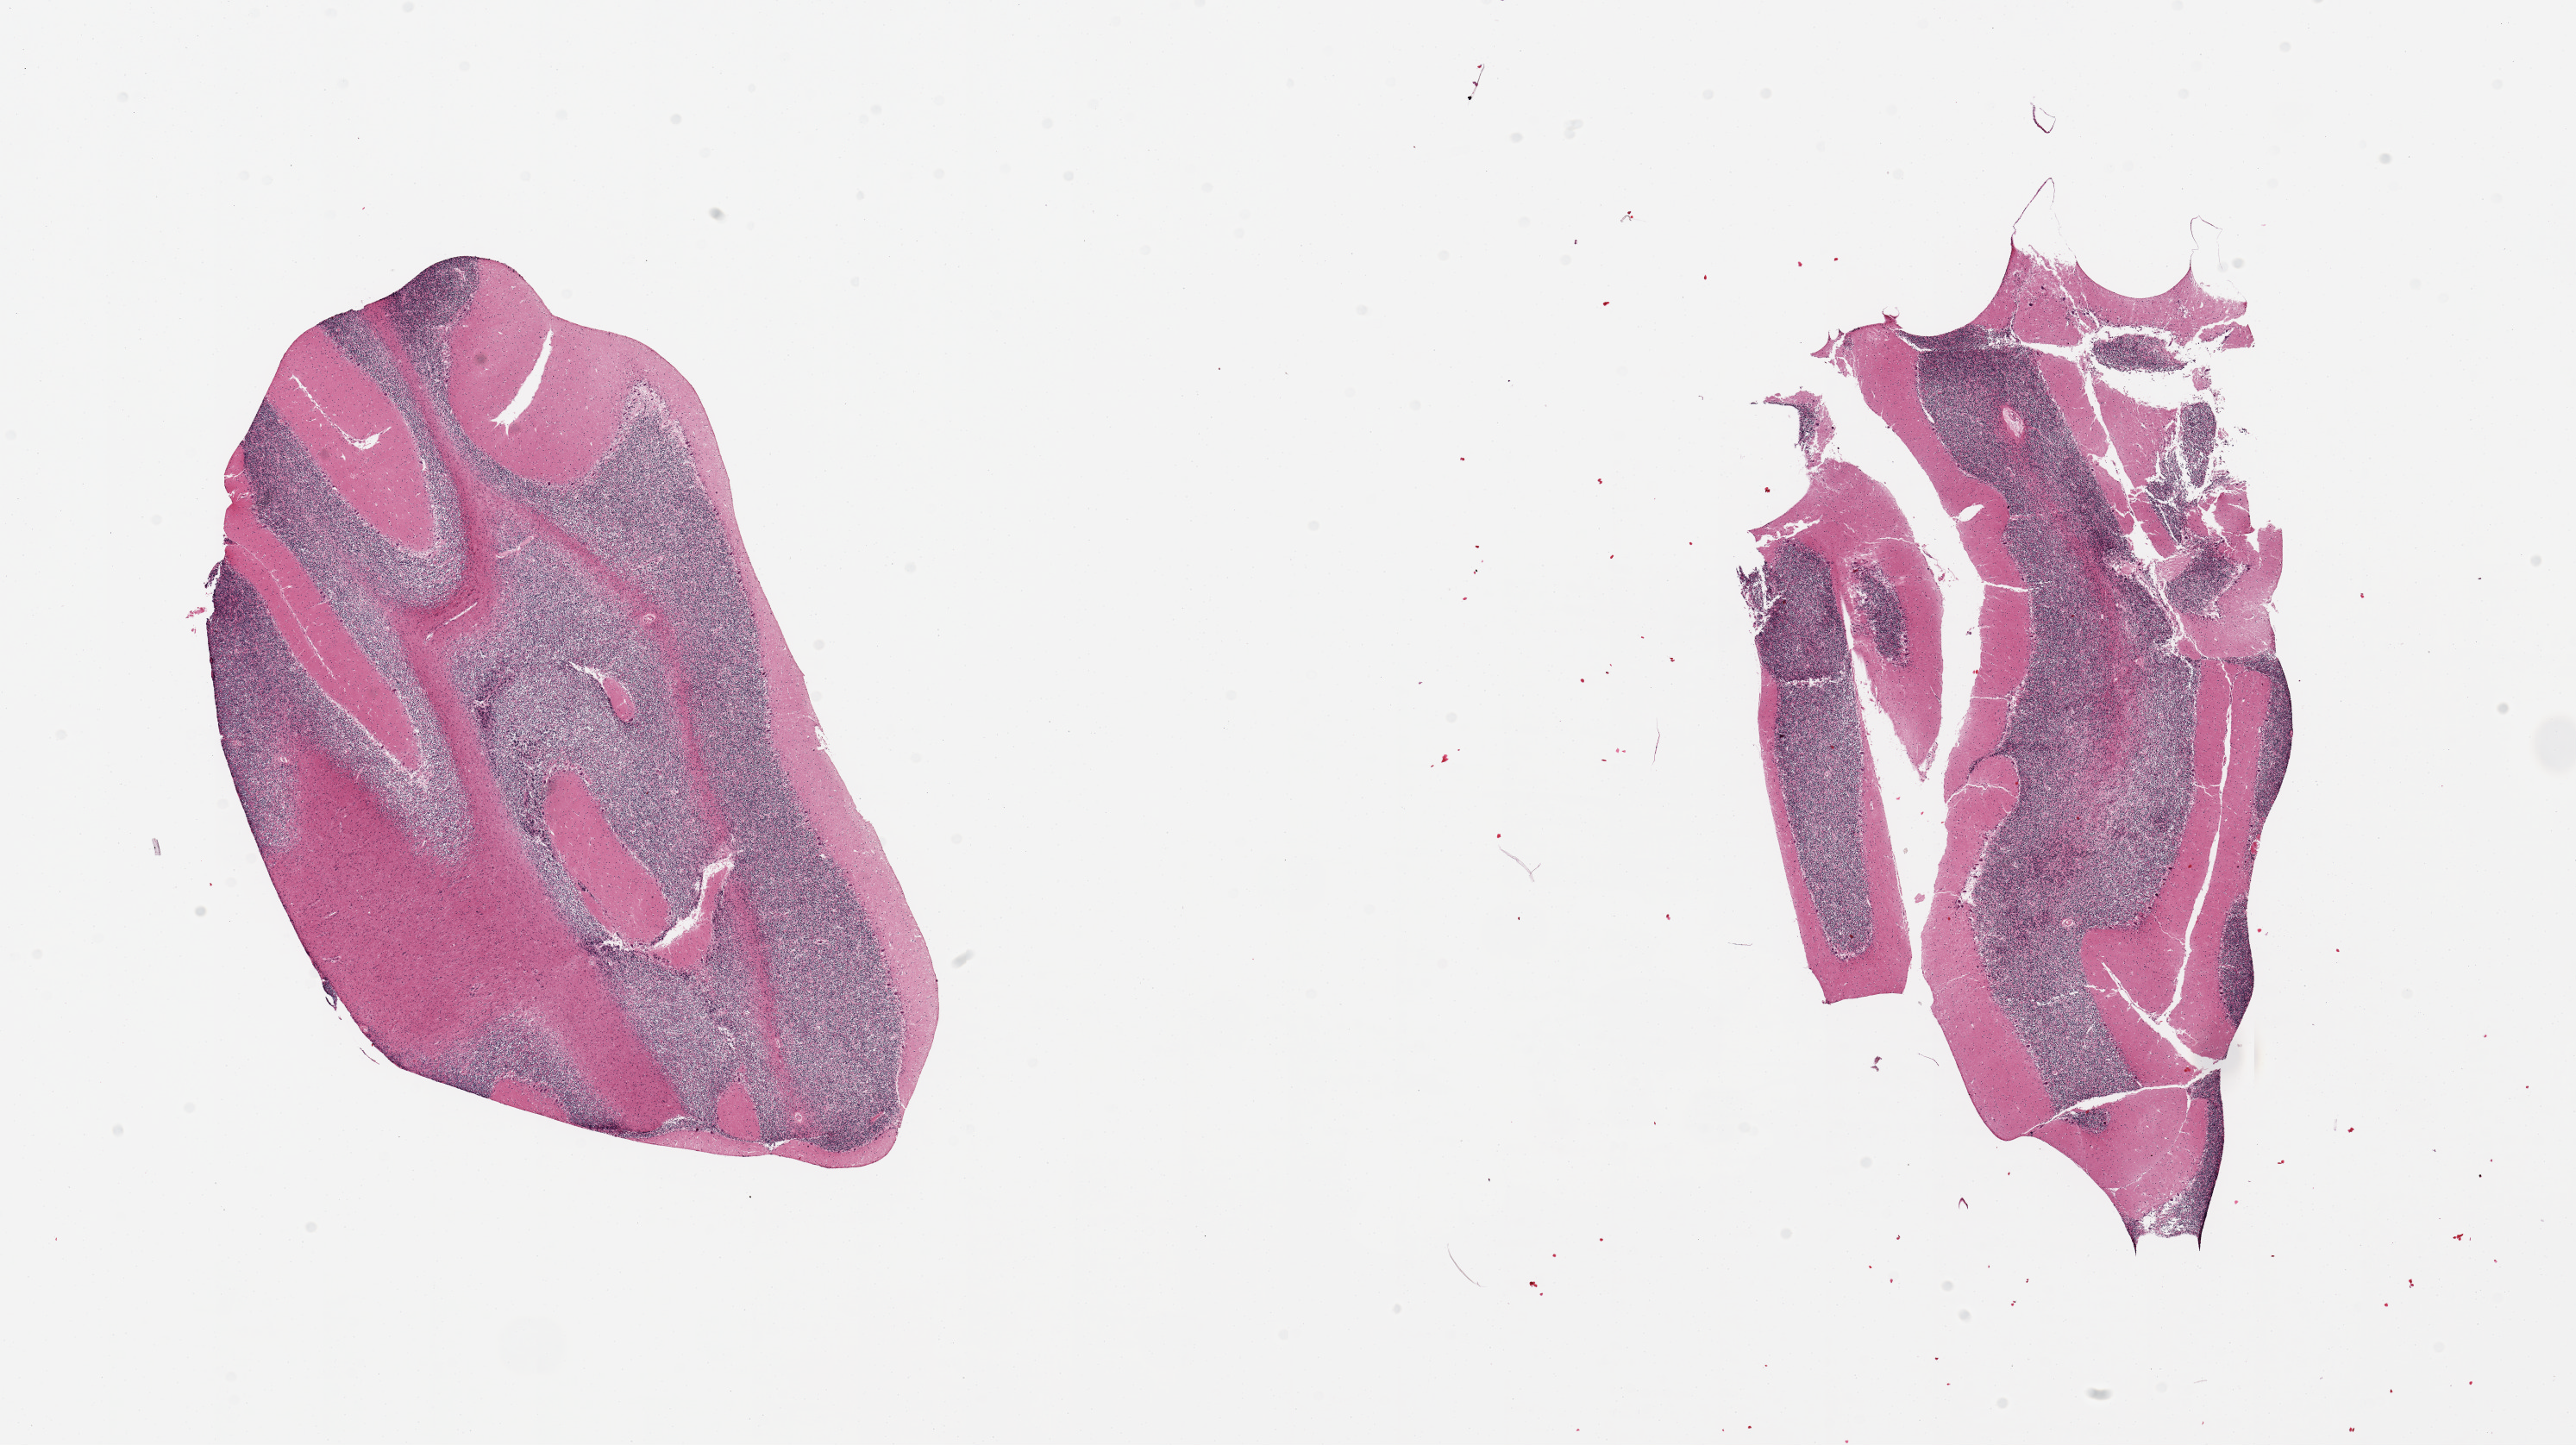
Digitized hematoxylin and eosin (H&E)-stained section — low-resolution overview of the scanned area, about 23.6 x 13.3 mm. PAXgene-fixed, paraffin-embedded tissue. Section of cerebellum (target tissue). Tissue donor sample. Donor sex: male.
Reviewer comment on this tissue sample: 2 pieces, no abnormalities.